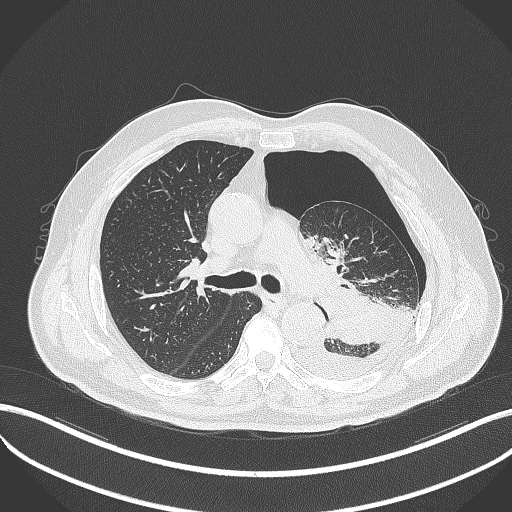
Chest CT, one axial slice; position 327 of 464 along the scan axis; reconstruction kernel B70f; 120 kVp; lung window (W 1500 / L -600 HU); 1 mm slice thickness; 512 × 512 image matrix. Male patient, age 76 years. From the clinical record (not read from this slice): clinical TNM (as recorded): T3 N0 M1b.
Structures marked on this image (rectangle marked by the reading radiologist):
- lung tumour (recorded histology: adenocarcinoma): bounding box (x1, y1, x2, y2) in pixels: (315, 282, 397, 346)